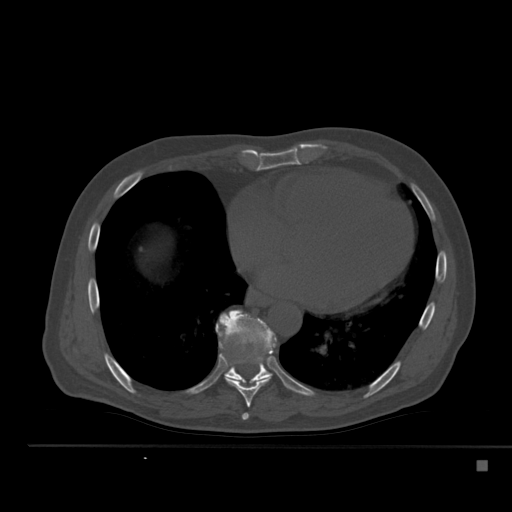
CT including the spine, one axial slice; slice 300 of 517 in the series (ordered by position); reconstruction kernel Br40s; 120 kVp; bone window (W 1800 / L 400 HU); 1.5 mm slice thickness; 512 × 512 image matrix, field of view 408 × 408 mm. Male patient, age 70 years. Case-level facts recorded for this patient, not image findings: primary cancer: renal; vertebrae with lytic lesions (as recorded): T4, T6, T10, T12, L3, L4, L5.
Annotated regions visible in this slice (semi-automatic segmentation, software-assisted and operator-edited):
- T7 vertebra: bounding box [x1, y1, x2, y2] px = [242, 413, 249, 420]
- T8 vertebra: [216, 324, 271, 407]
- T9 vertebra: [216, 310, 276, 383]